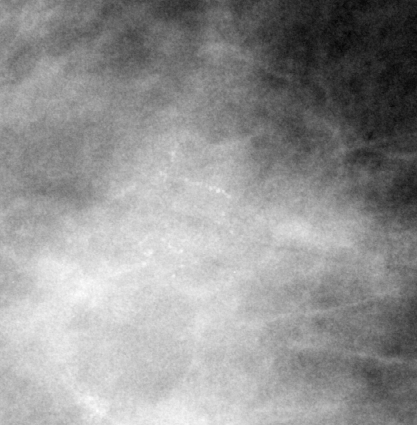
Crop from a digitized film mammogram around one marked abnormality, right breast, MLO view, BI-RADS breast density category 3 (scale 1–4).
- Calcifications, morphology amorphous, distribution clustered; BI-RADS assessment category 4; pathology result (as recorded, not read from the image): benign.